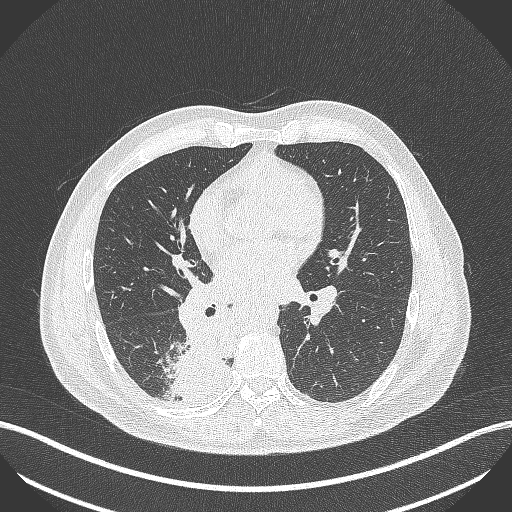
Chest CT, one axial slice. Slice 231 of 451 in the series (ordered by position). 100 kVp. Lung window (W 1500 / L -600 HU). 1 mm slice thickness. 512 × 512 image matrix, field of view 400 × 400 mm. Male patient, age 61 years. Case-level facts recorded for this patient, not image findings: clinical TNM (as recorded): T1 N0 M0; histopathological grade: G3.
Structures marked on this image (bounding box drawn by a radiologist):
- lung tumour (recorded histology: small cell carcinoma): bounding box <164,308,232,401> (left, top, right, bottom; pixels)